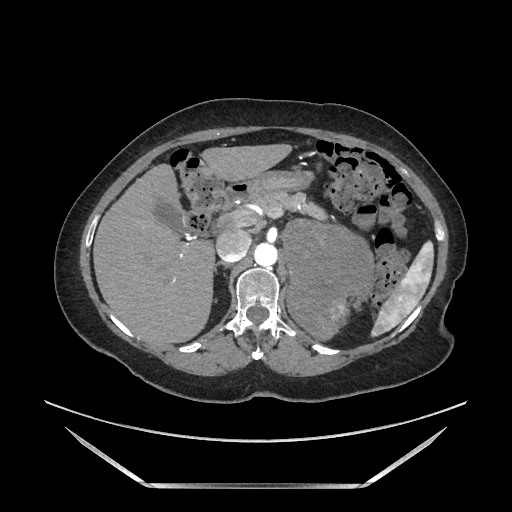
Contrast-enhanced abdominal CT, one axial slice. Slice 113 of 205 in the series (ordered by position). Soft-tissue window (W 400 / L 40 HU). 1.25 mm slice thickness. 512 × 512 image matrix. Female patient. From the clinical record (not read from this slice): diagnosis: adrenocortical carcinoma; tumour side: left adrenal; tumour size at pathology: 12.5 cm; Ki-67 index: 39 %.
Annotated regions visible in this slice (semi-automatic segmentation, software-assisted and operator-edited):
- mass: bounding box (x1, y1, x2, y2) in pixels: (286, 221, 372, 335)